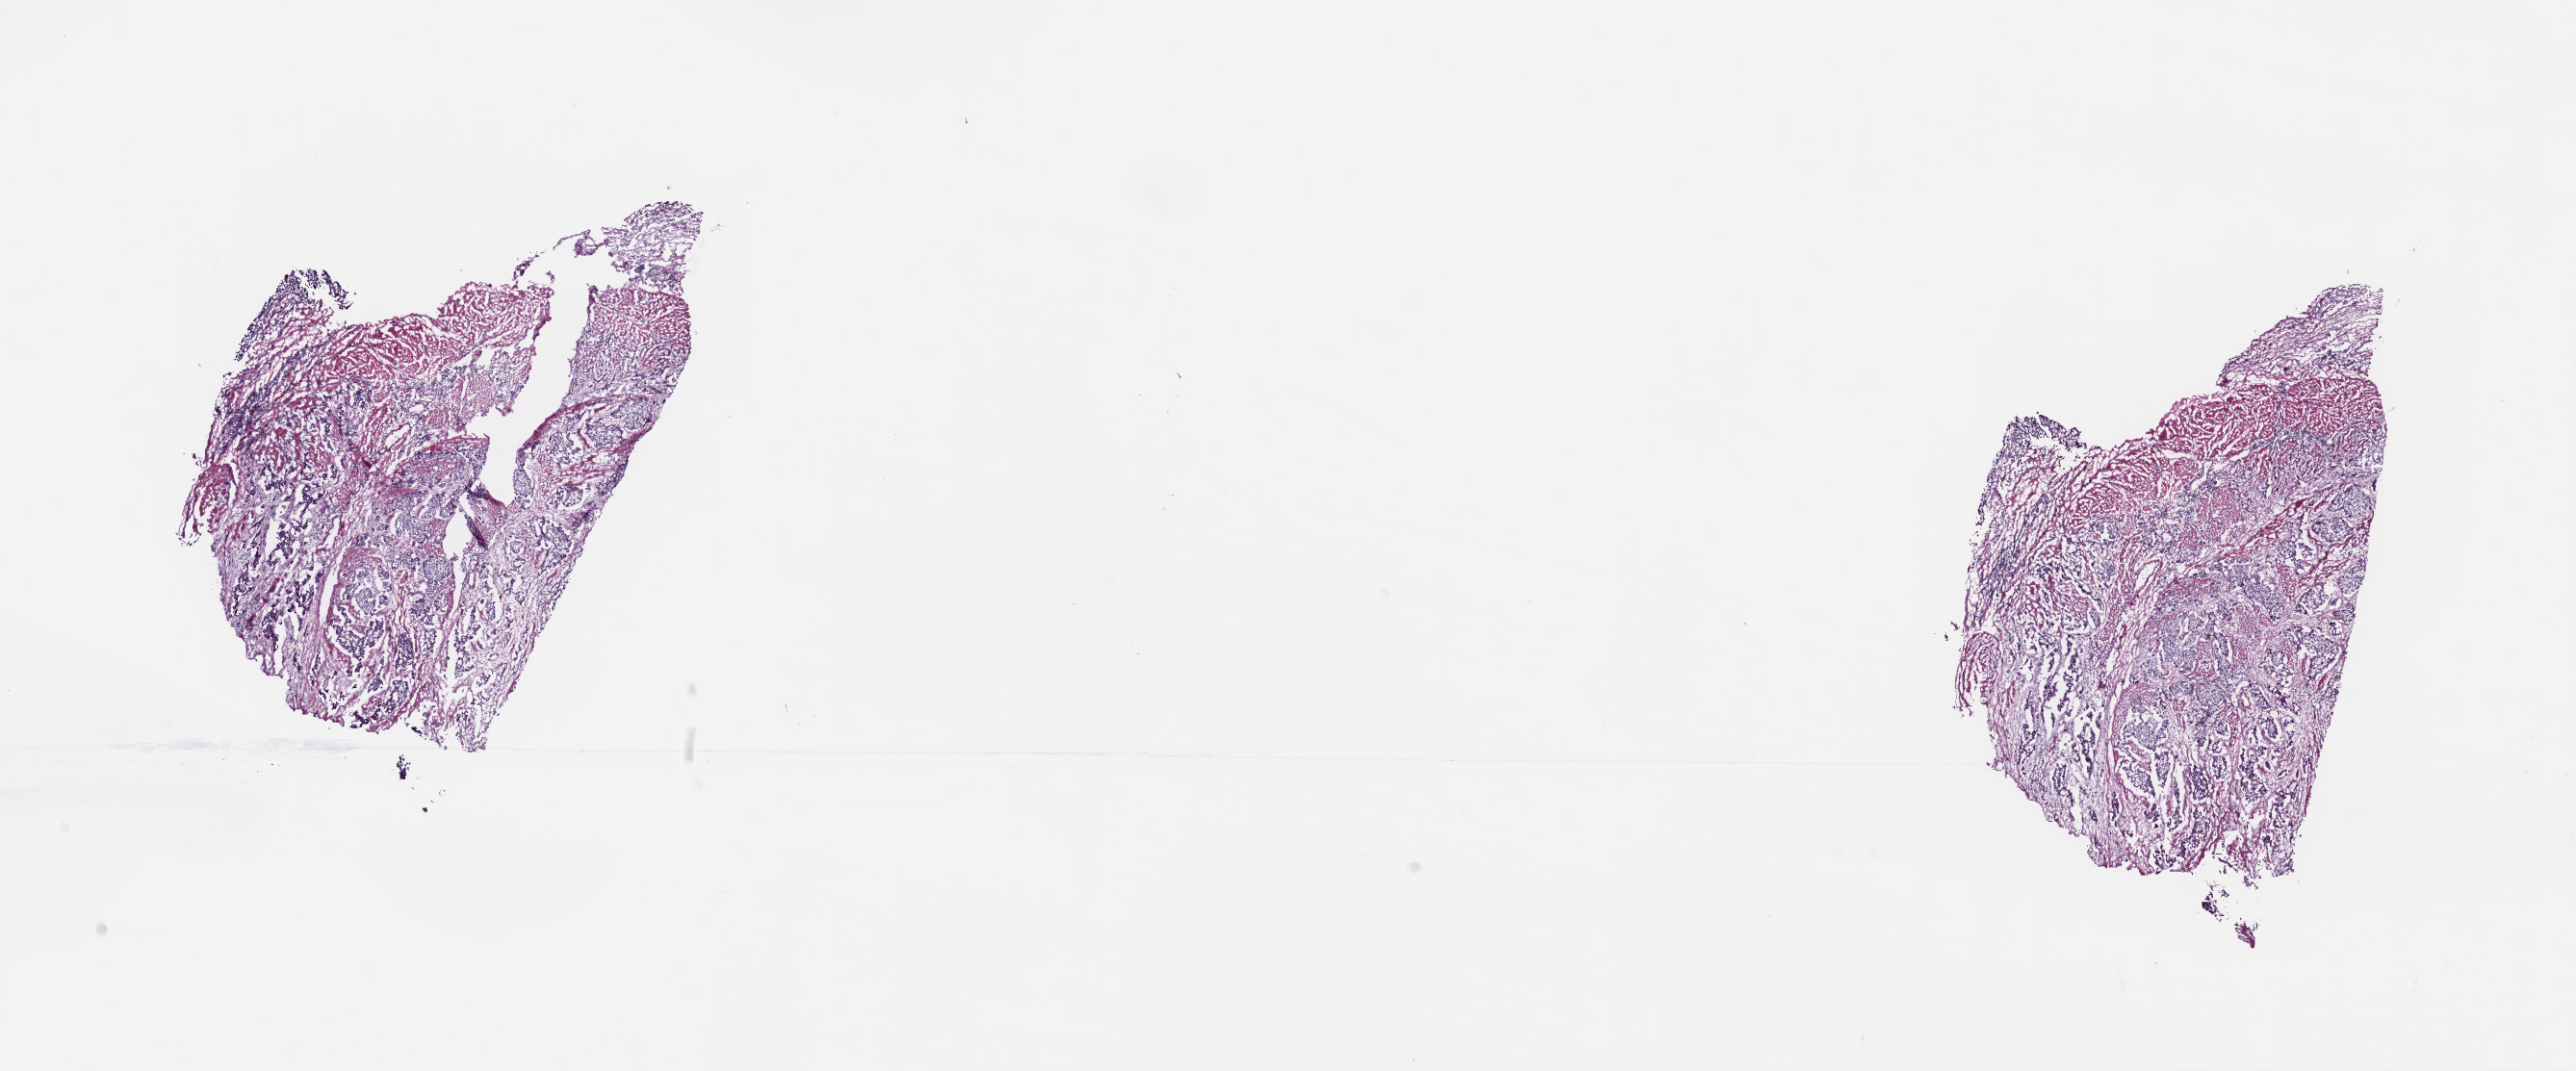
Digitized H&E-stained tissue section (whole slide), low-resolution overview of the scanned area, about 21.6 x 9.0 mm; frozen section from the top of the tissue portion; sample: primary tumour, bladder. Patient: male, age at initial diagnosis 82 years. Histologic grade: high grade. Composition of this section per pathologist review: tumour cells 100%, tumour nuclei 70%, normal cells 0%, stromal cells 0%, necrosis 0%. Infiltration values recorded for this section: lymphocyte infiltration 3%, monocyte infiltration 0%, neutrophil infiltration 0%.
Histologic diagnosis: Transitional cell carcinoma. AJCC pathologic stage: III (7th edition).